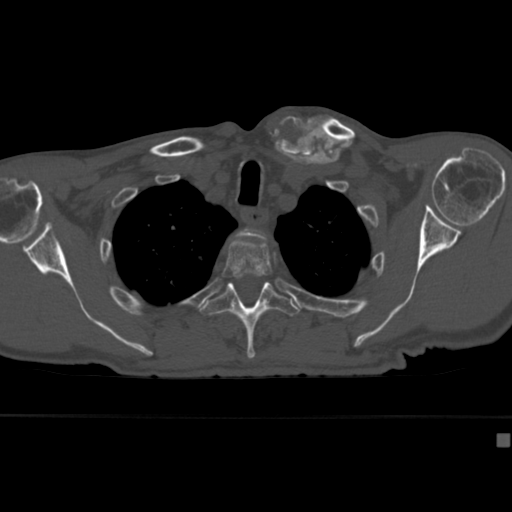
CT including the spine, one axial slice; slice 327 of 430 in the series (ordered by position); reconstruction kernel Br40s; 120 kVp; bone window (W 1800 / L 400 HU); 1.5 mm slice thickness; 512 × 512 image matrix, field of view 337 × 337 mm. Male patient, age 64 years. From the clinical record (not read from this slice): primary cancer: uterus.
Outlined on this slice (semi-automatic segmentation, software-assisted and operator-edited):
- T2 vertebra: bounding box (x1, y1, x2, y2) in pixels: (237, 228, 267, 240)
- T3 vertebra: (222, 239, 272, 279)
- T4 vertebra: (202, 281, 300, 359)